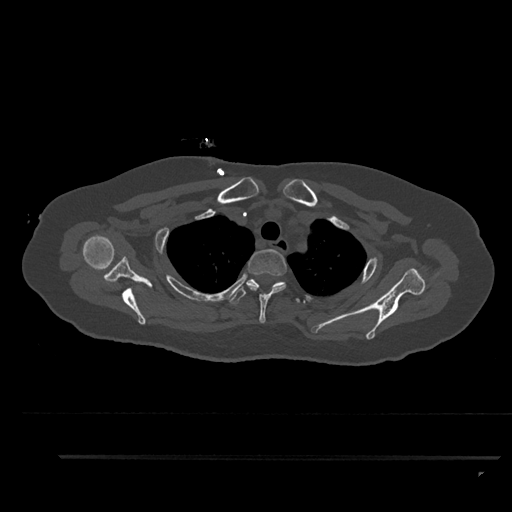
CT including the spine, one axial slice; 120 kVp; bone window (W 1800 / L 400 HU); 512 × 512 image matrix. Female patient, age 44 years. From the clinical record (not read from this slice): primary cancer: renal.
Annotated regions visible in this slice (semi-automatically segmented with operator editing):
- T1 vertebra: box from (x=279, y=284) to (x=286, y=287) px
- T2 vertebra: (x=246, y=249)–(x=287, y=323)
- T3 vertebra: (x=229, y=279)–(x=300, y=304)